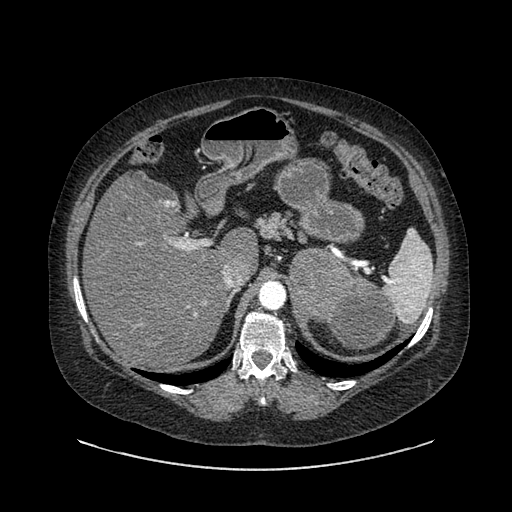
Contrast-enhanced abdominal CT, one axial slice. Position 604 of 769 along the scan axis. Reconstruction kernel SOFT. 120 kVp. Intravenous contrast given. Soft-tissue window (W 400 / L 40 HU). 512 × 512 image matrix. Female patient, age 61 years. Case-level facts recorded for this patient, not image findings: diagnosis: adrenocortical carcinoma; tumour side: left adrenal; tumour size at pathology: 13 cm.
Outlined on this slice (semi-automatically segmented with operator editing):
- mass: bounding box (x1, y1, x2, y2) in pixels: (289, 250, 395, 349)